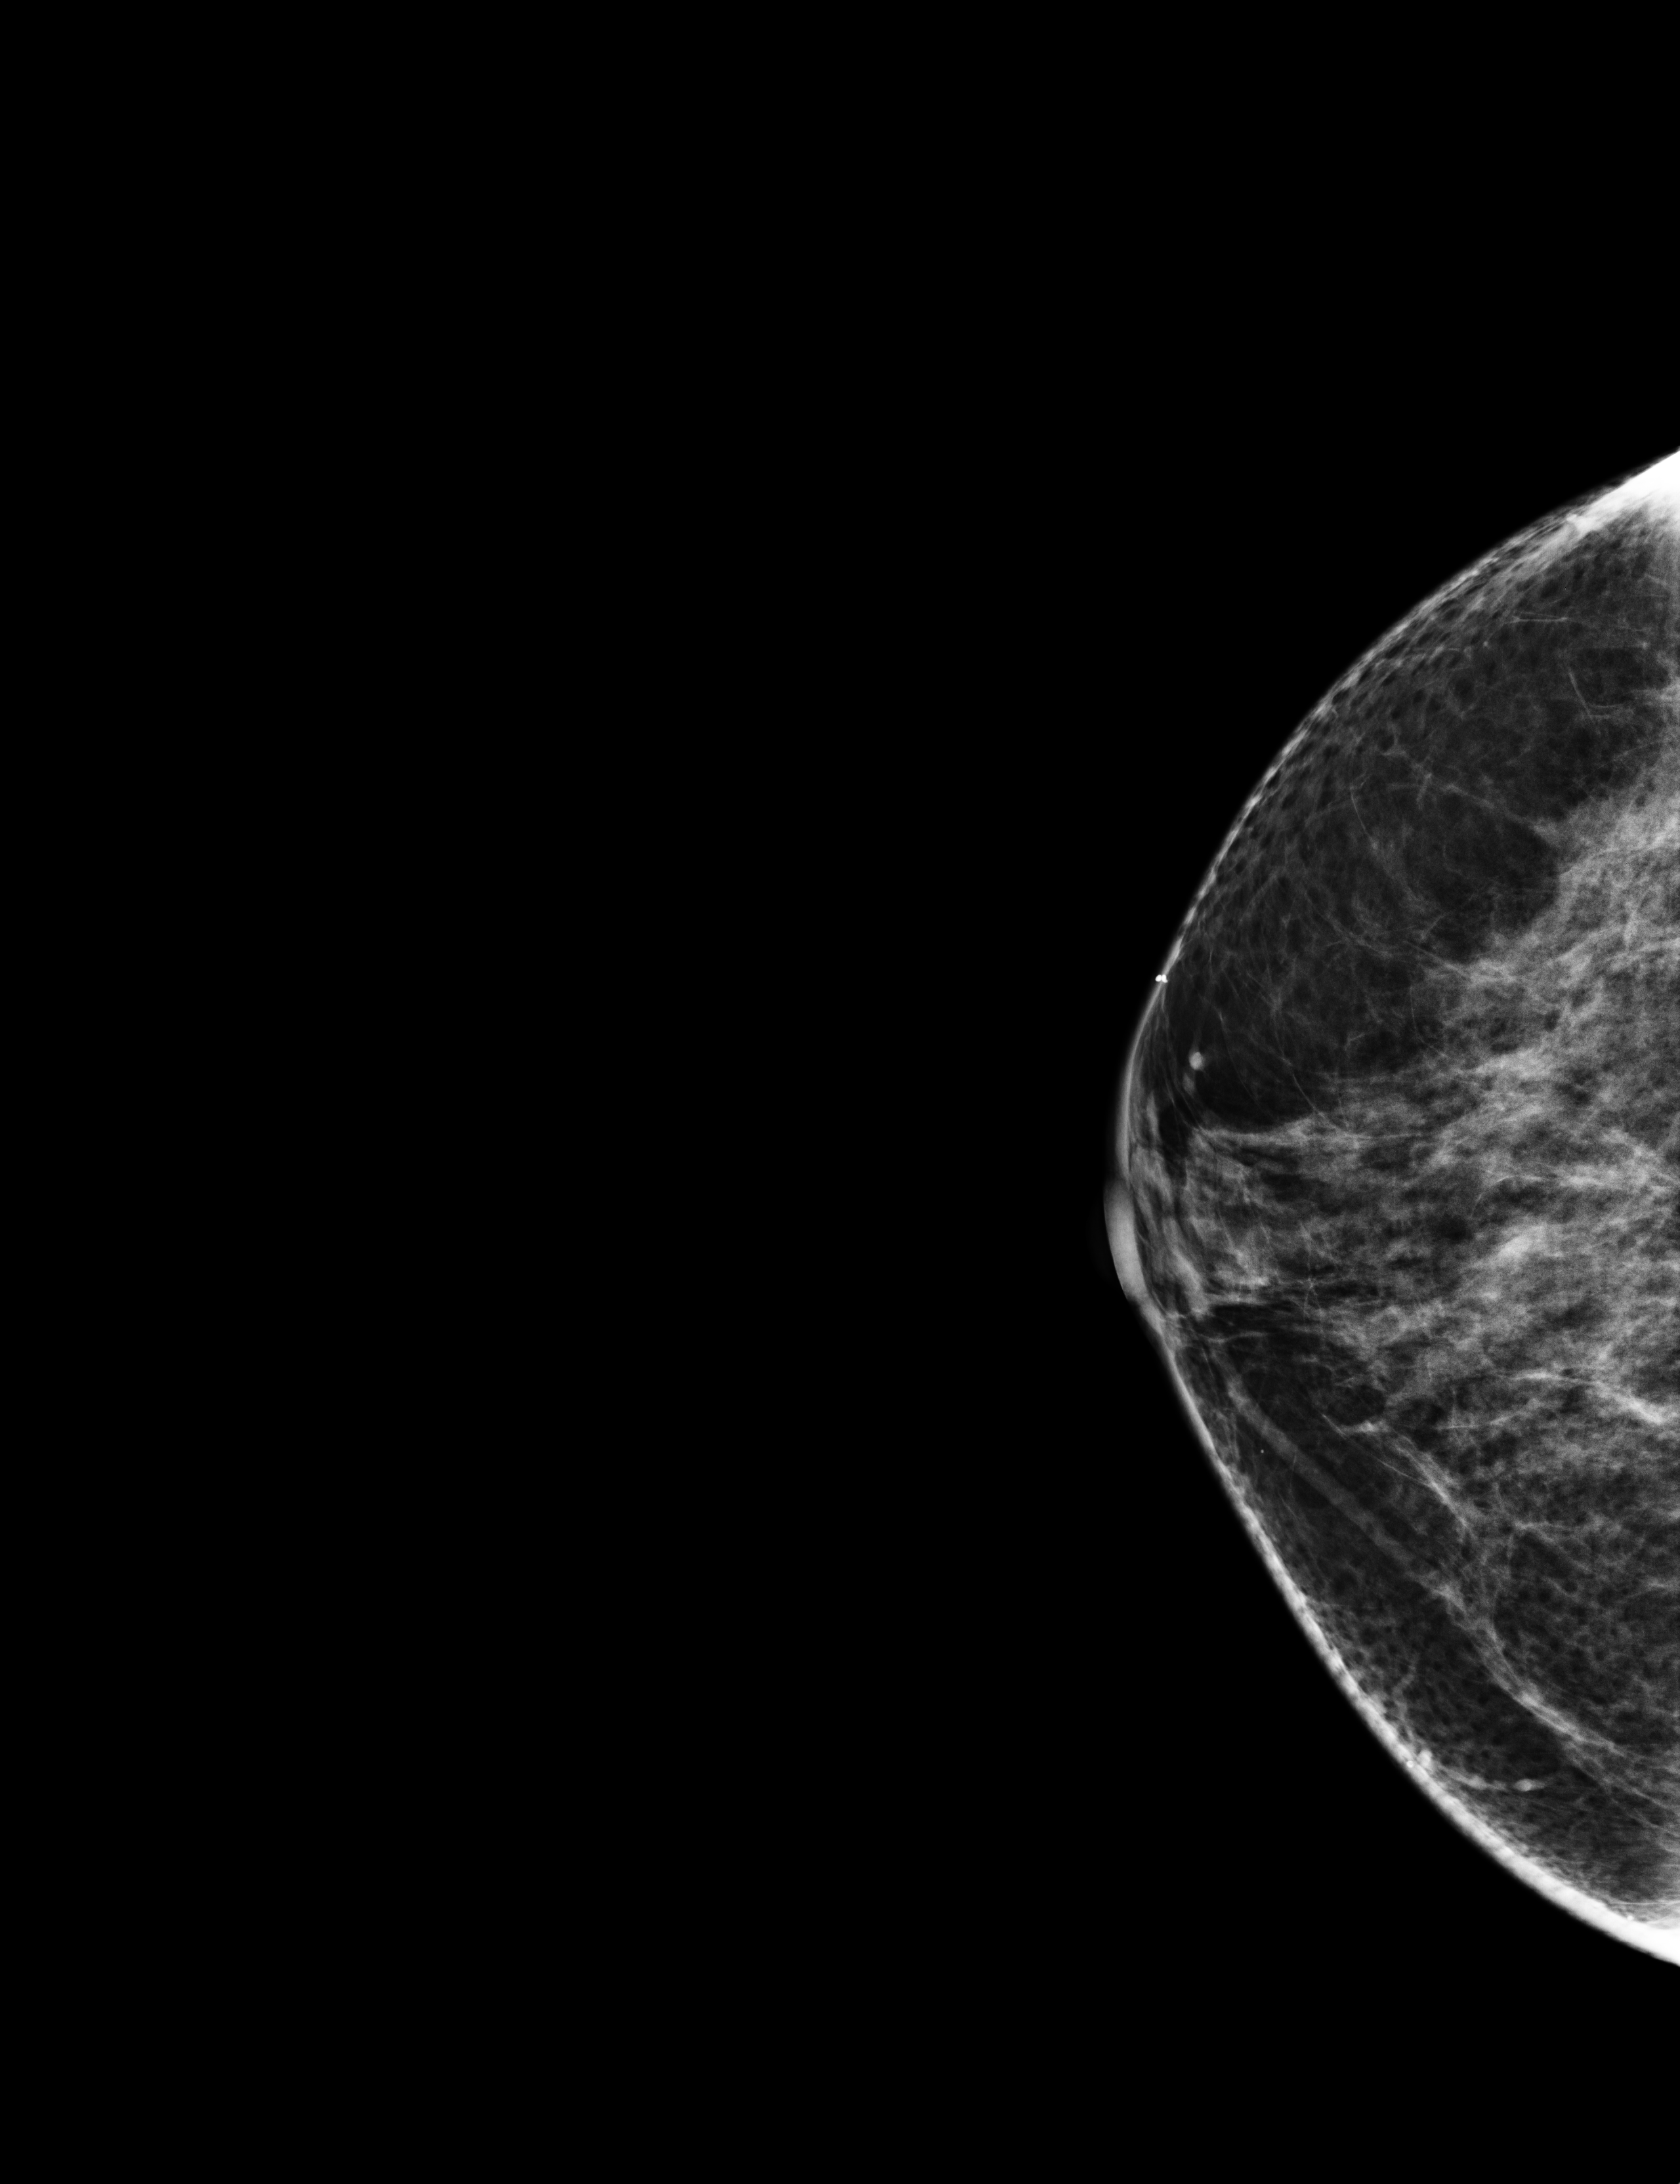
Screening examination; system: Selenia Dimensions.
Image type: full-field digital mammogram. Breast: right. Projection: cranio-caudal projection.